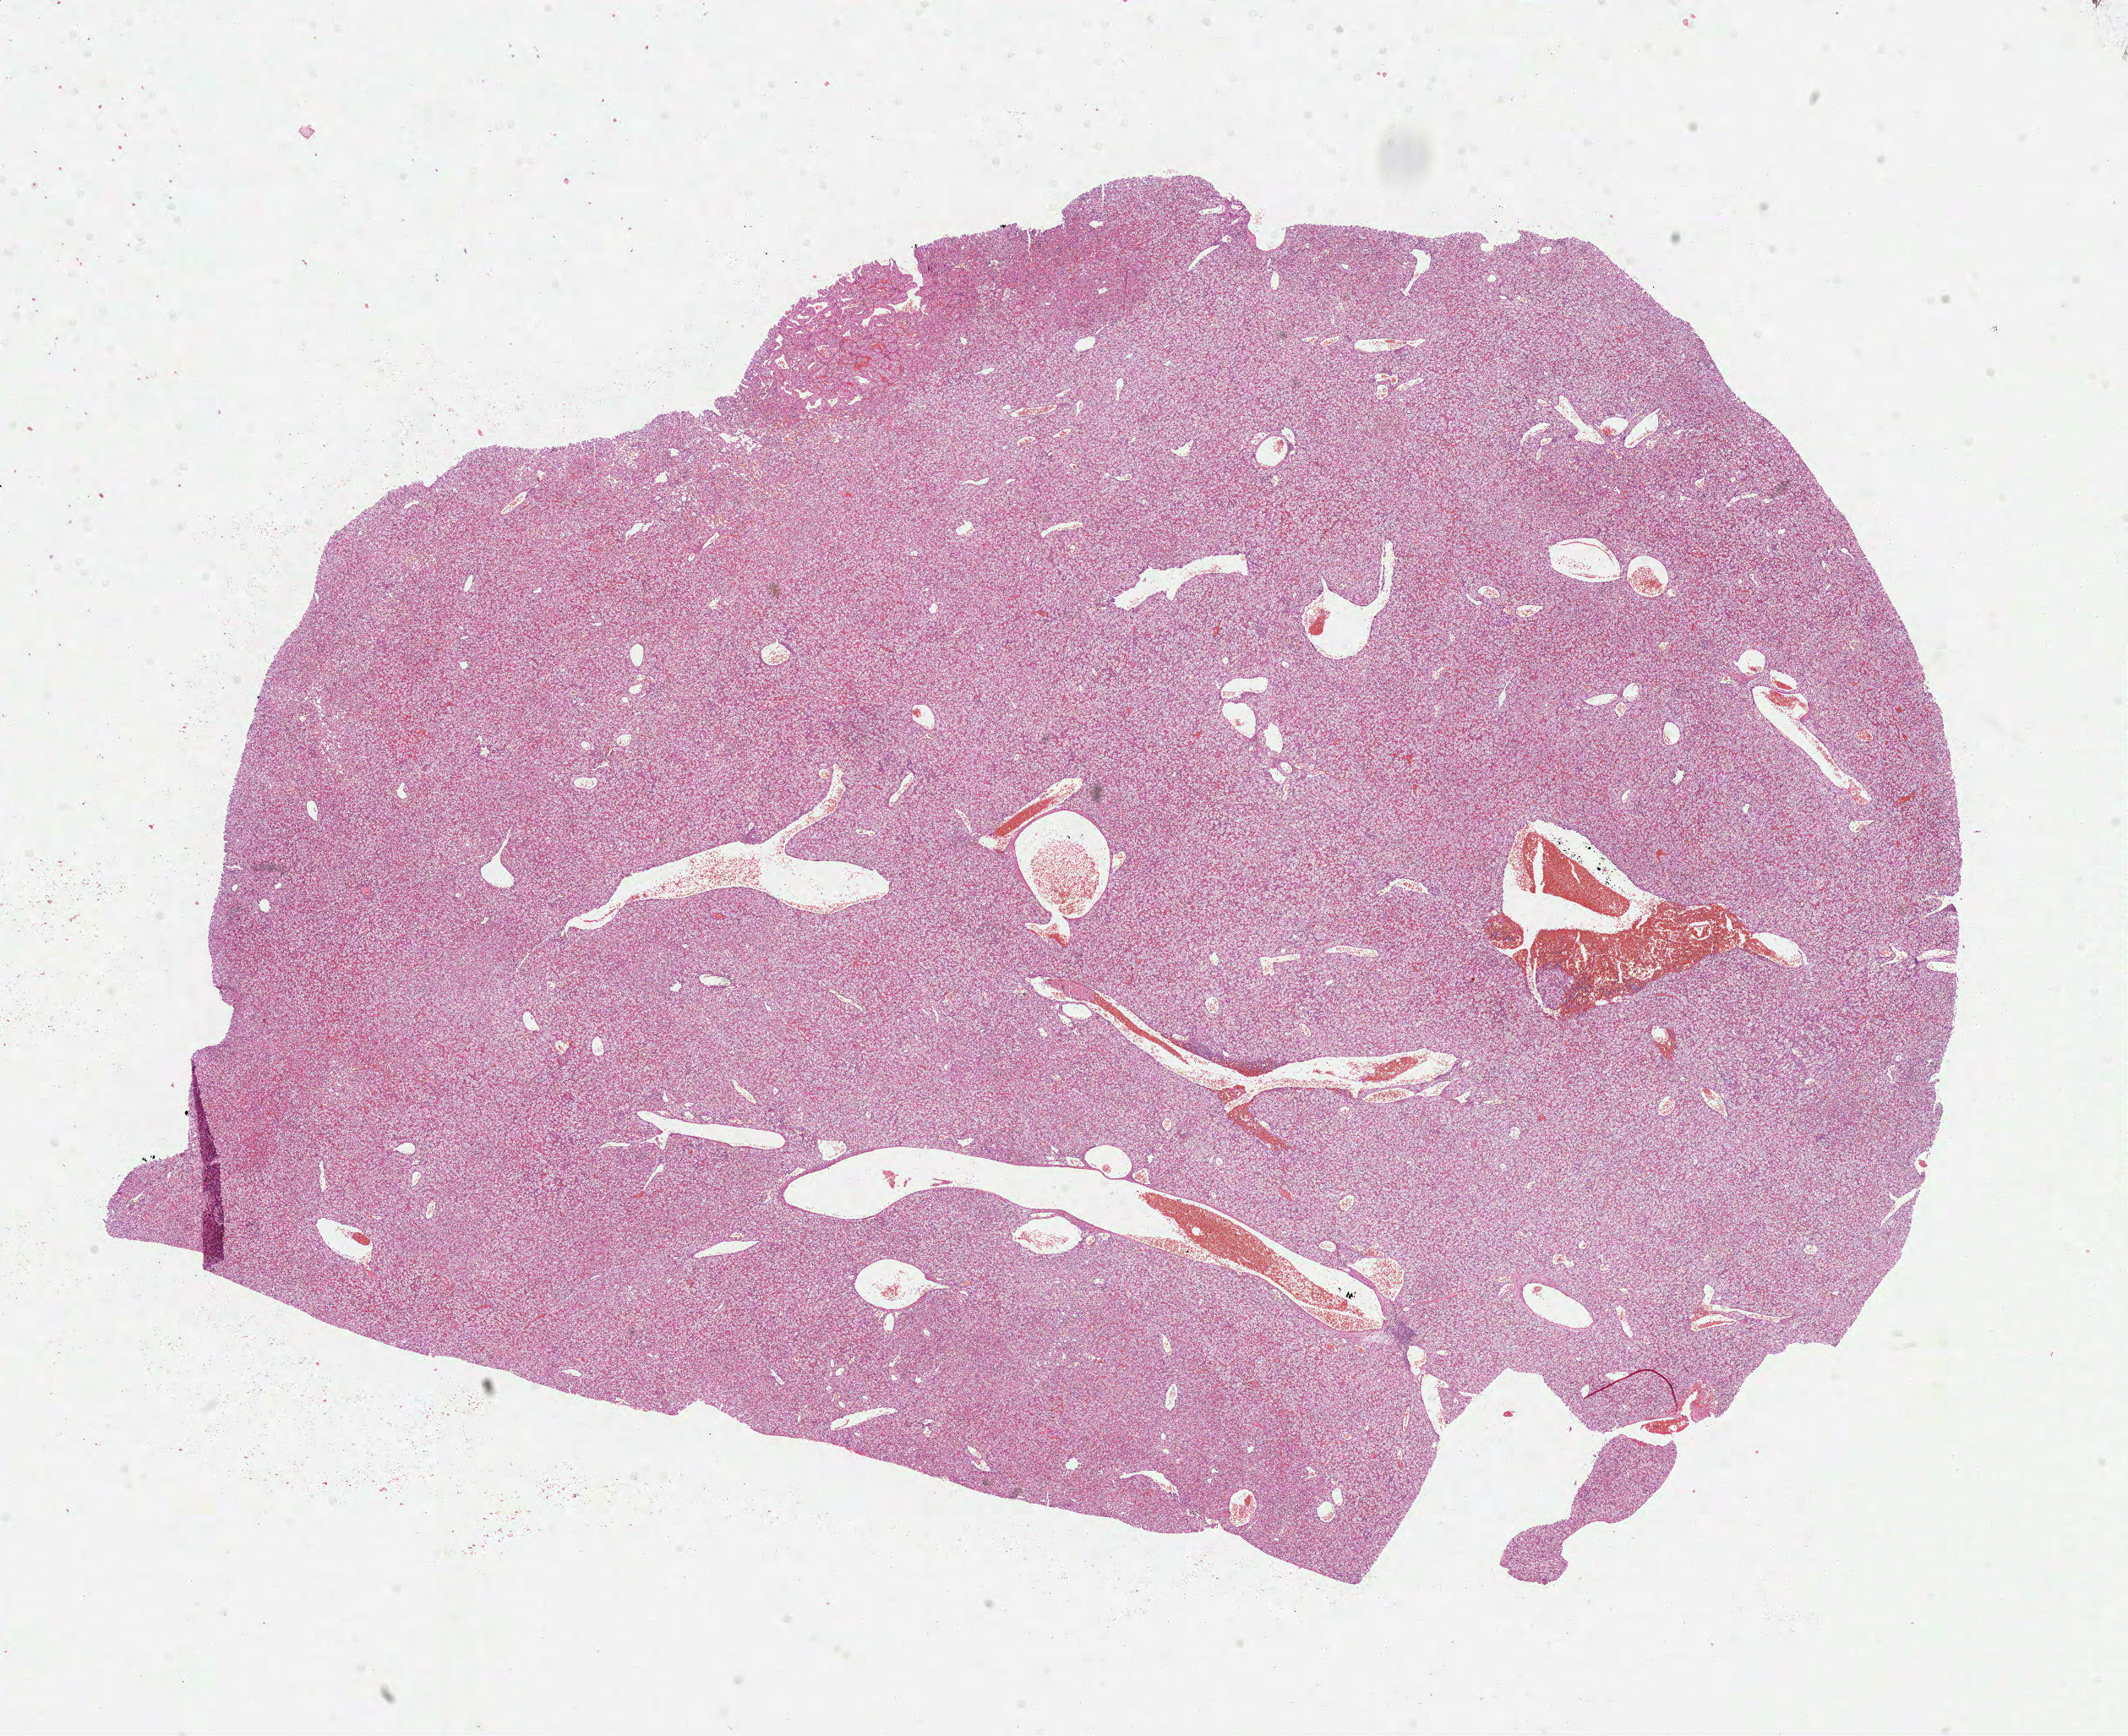
Whole-slide histology image, Hematoxylin and eosin (H&E) stained — low-resolution overview of the scanned area, about 20.3 x 16.6 mm (slide scanned at 40x), formalin-fixed paraffin-embedded (FFPE) diagnostic section, primary tumour sample from the kidney. Male, age 47 years at initial diagnosis. Histologic grade: G1 (well differentiated).
• diagnosis: Clear cell adenocarcinoma, NOS
• AJCC pathologic stage: I